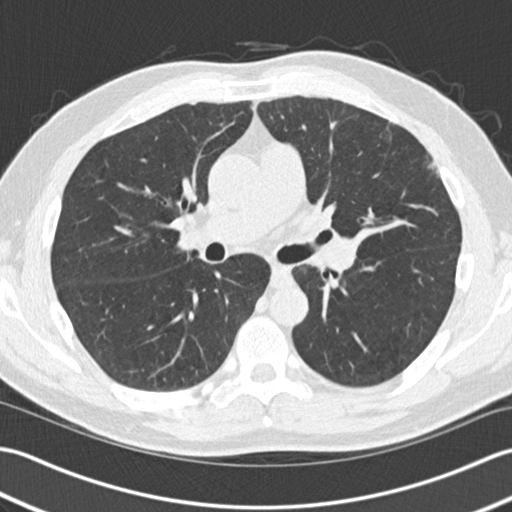
Low-dose screening chest CT, one axial slice; slice 76 of 140 in the series (ordered by position); 120 kVp; lung window (W 1500 / L -600 HU); 2 mm slice thickness; 512 × 512 image matrix, field of view 352 × 352 mm.
Outlined on this slice (manually delineated by an expert):
- lesion 1 (tumor, upper lobe of left lung): box from (x=428, y=161) to (x=441, y=178) px